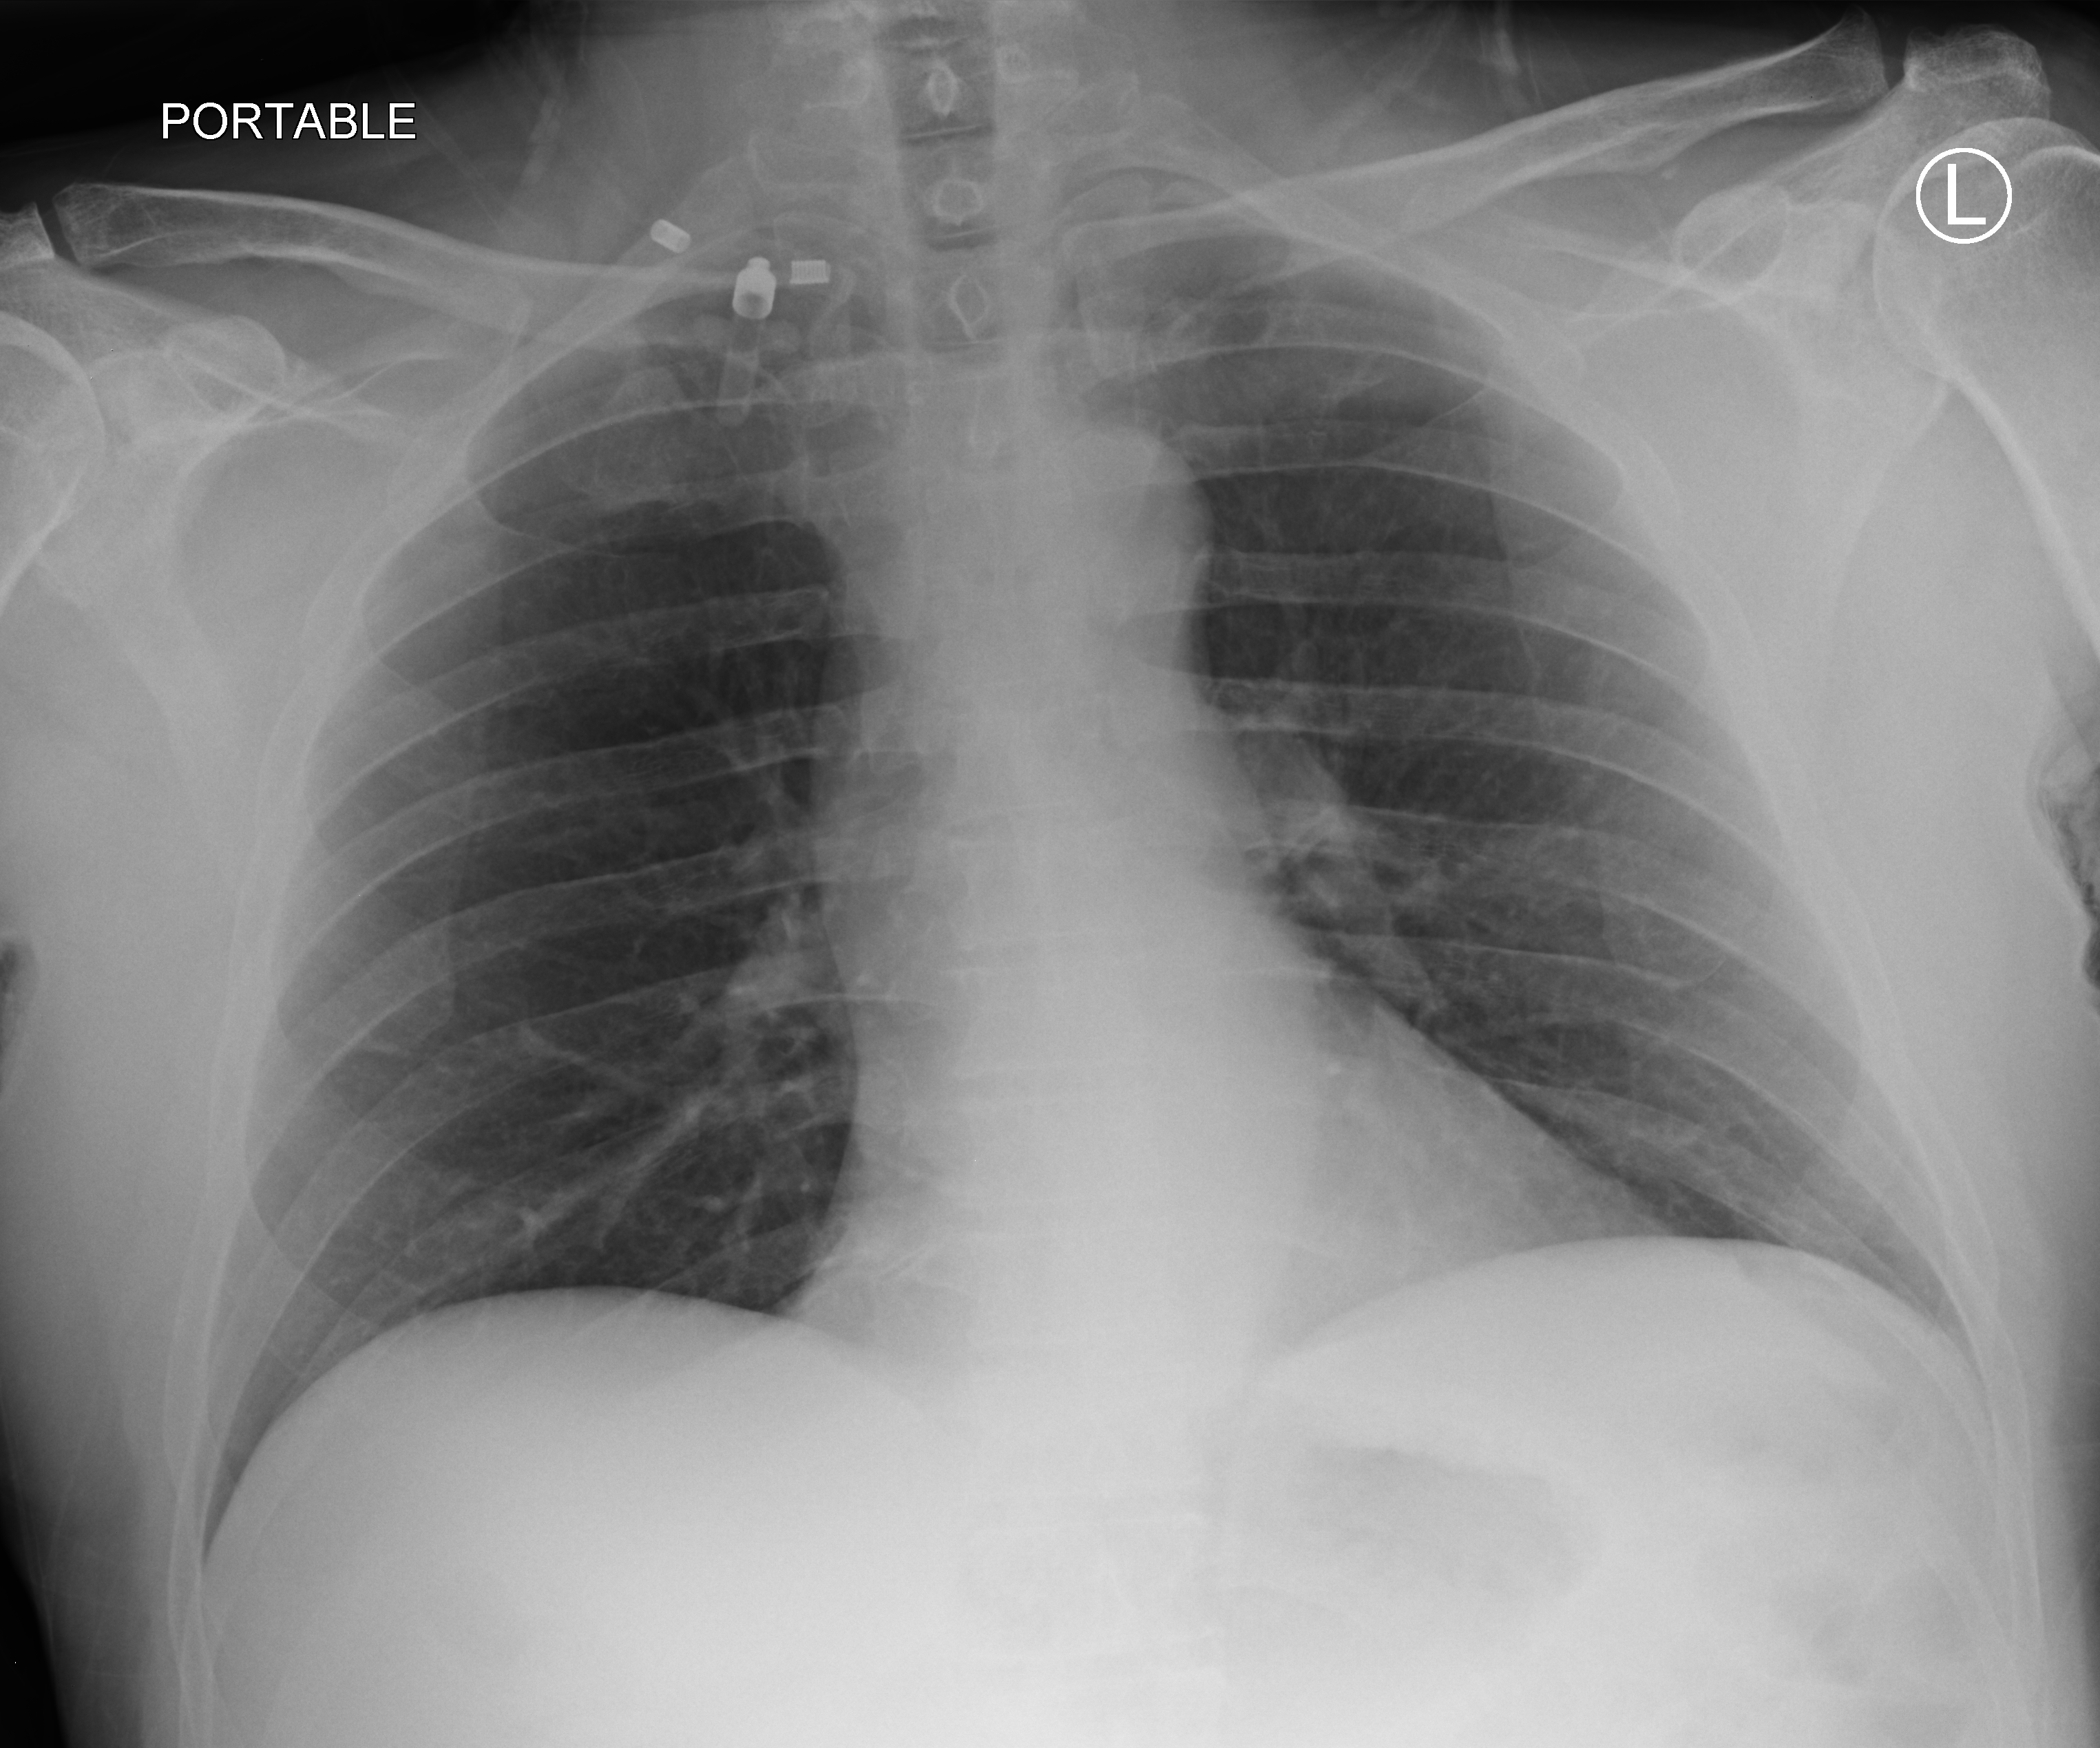
Chest X-ray (portable), anteroposterior (AP) projection. Male patient hospitalised with COVID-19, age 60–74 years.
From the hospital-stay record, not from the radiograph (when in the stay this image was taken is not recorded):
- mechanically ventilated during this hospital stay: no
- length of hospital stay: 1 day
- admitted to intensive care during this hospital stay: no